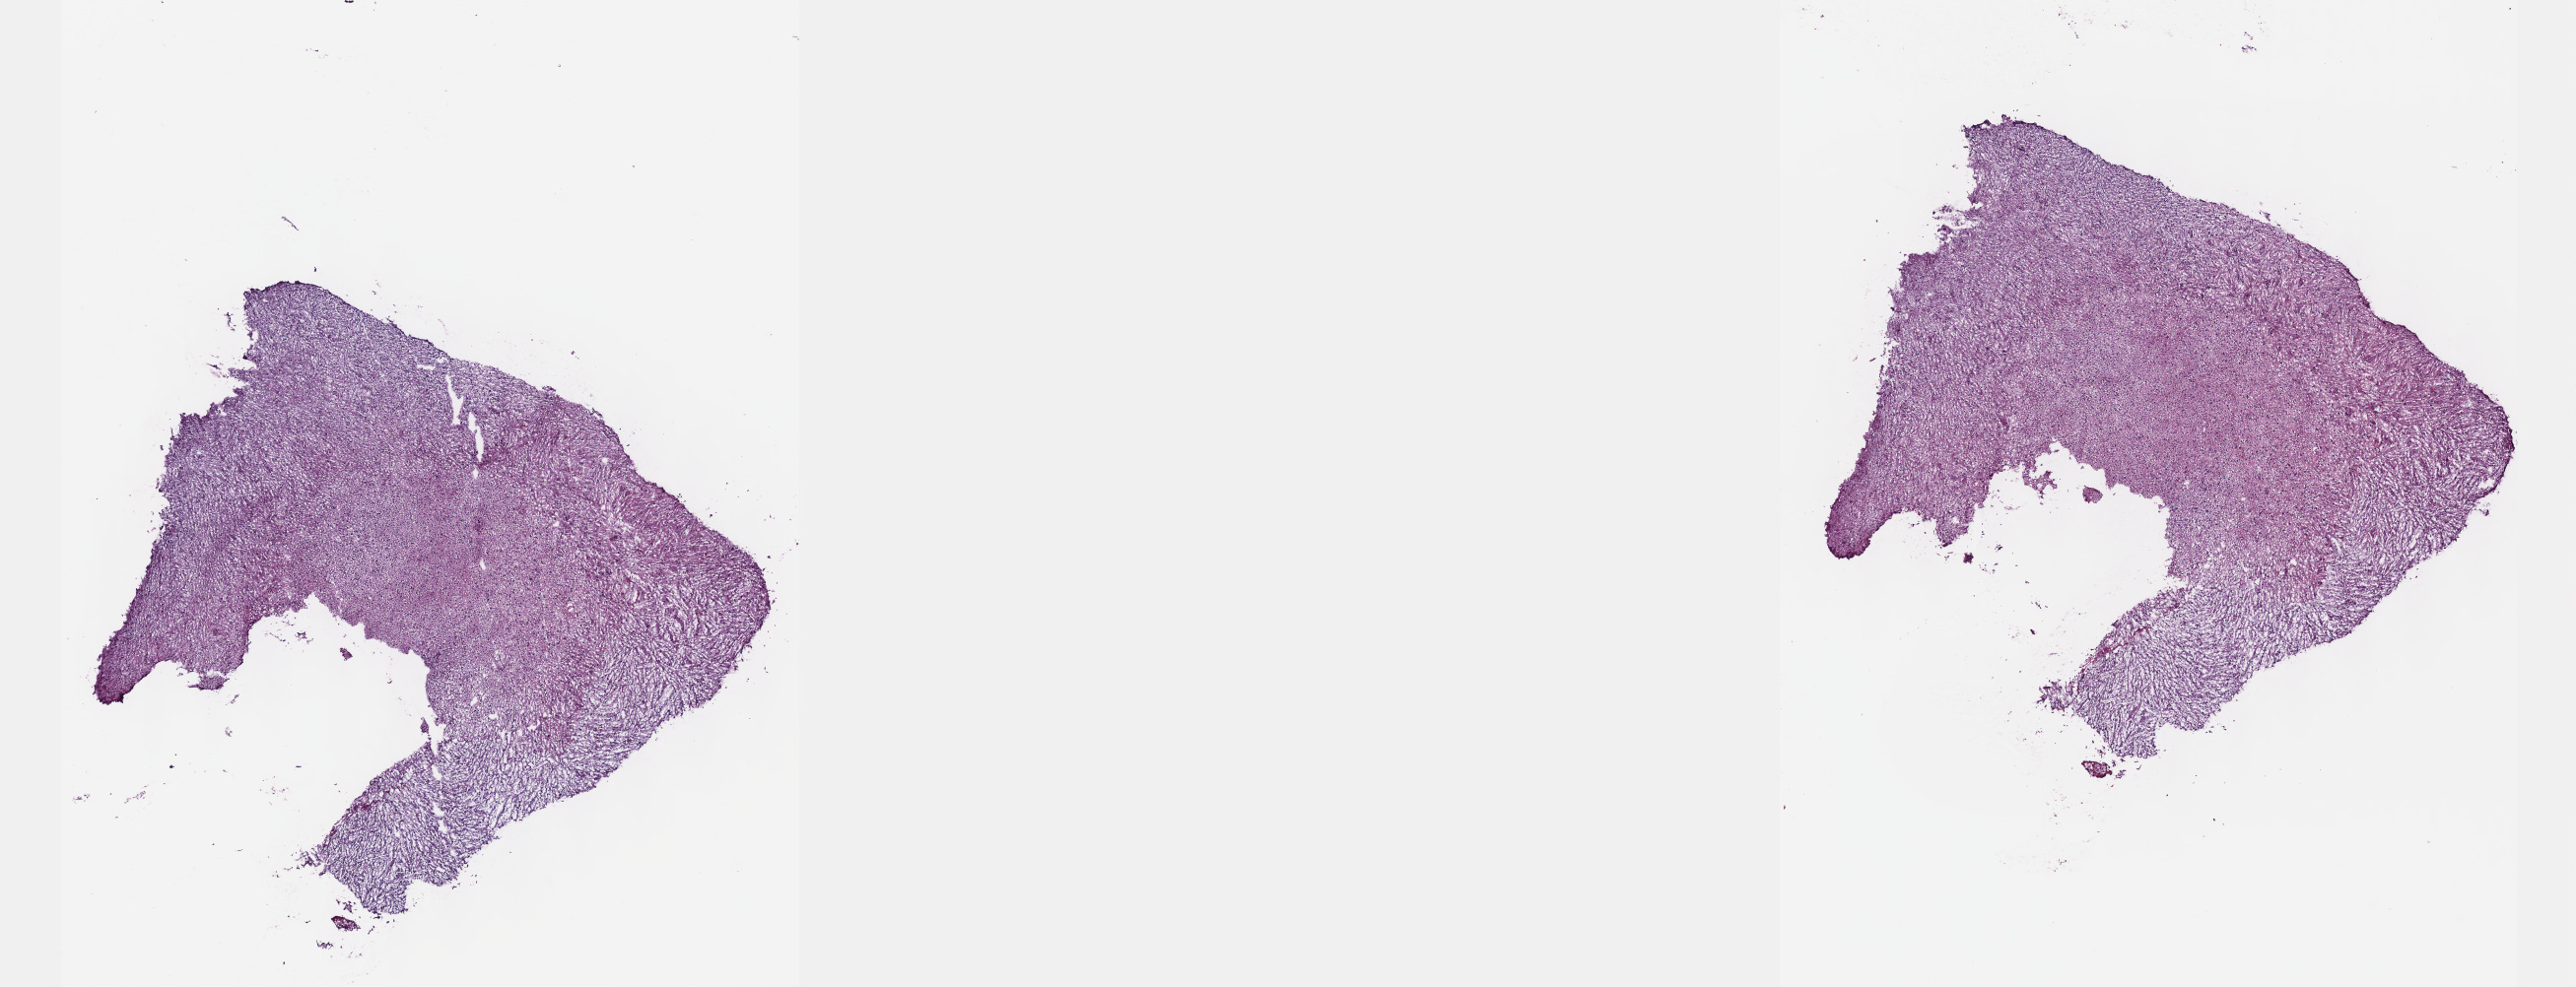
Digitized Hematoxylin and eosin (H&E) stained tissue section (whole slide), shown as a low-resolution overview of the whole scanned area (about 21.1 x 8.1 mm). Frozen section from the top of the tissue portion. Primary tumour sample from the brain. Patient: female, age at initial diagnosis 30 years. Slide review estimates, as recorded: tumour cells 50%, tumour nuclei 80%.
Diagnosis: Glioblastoma.